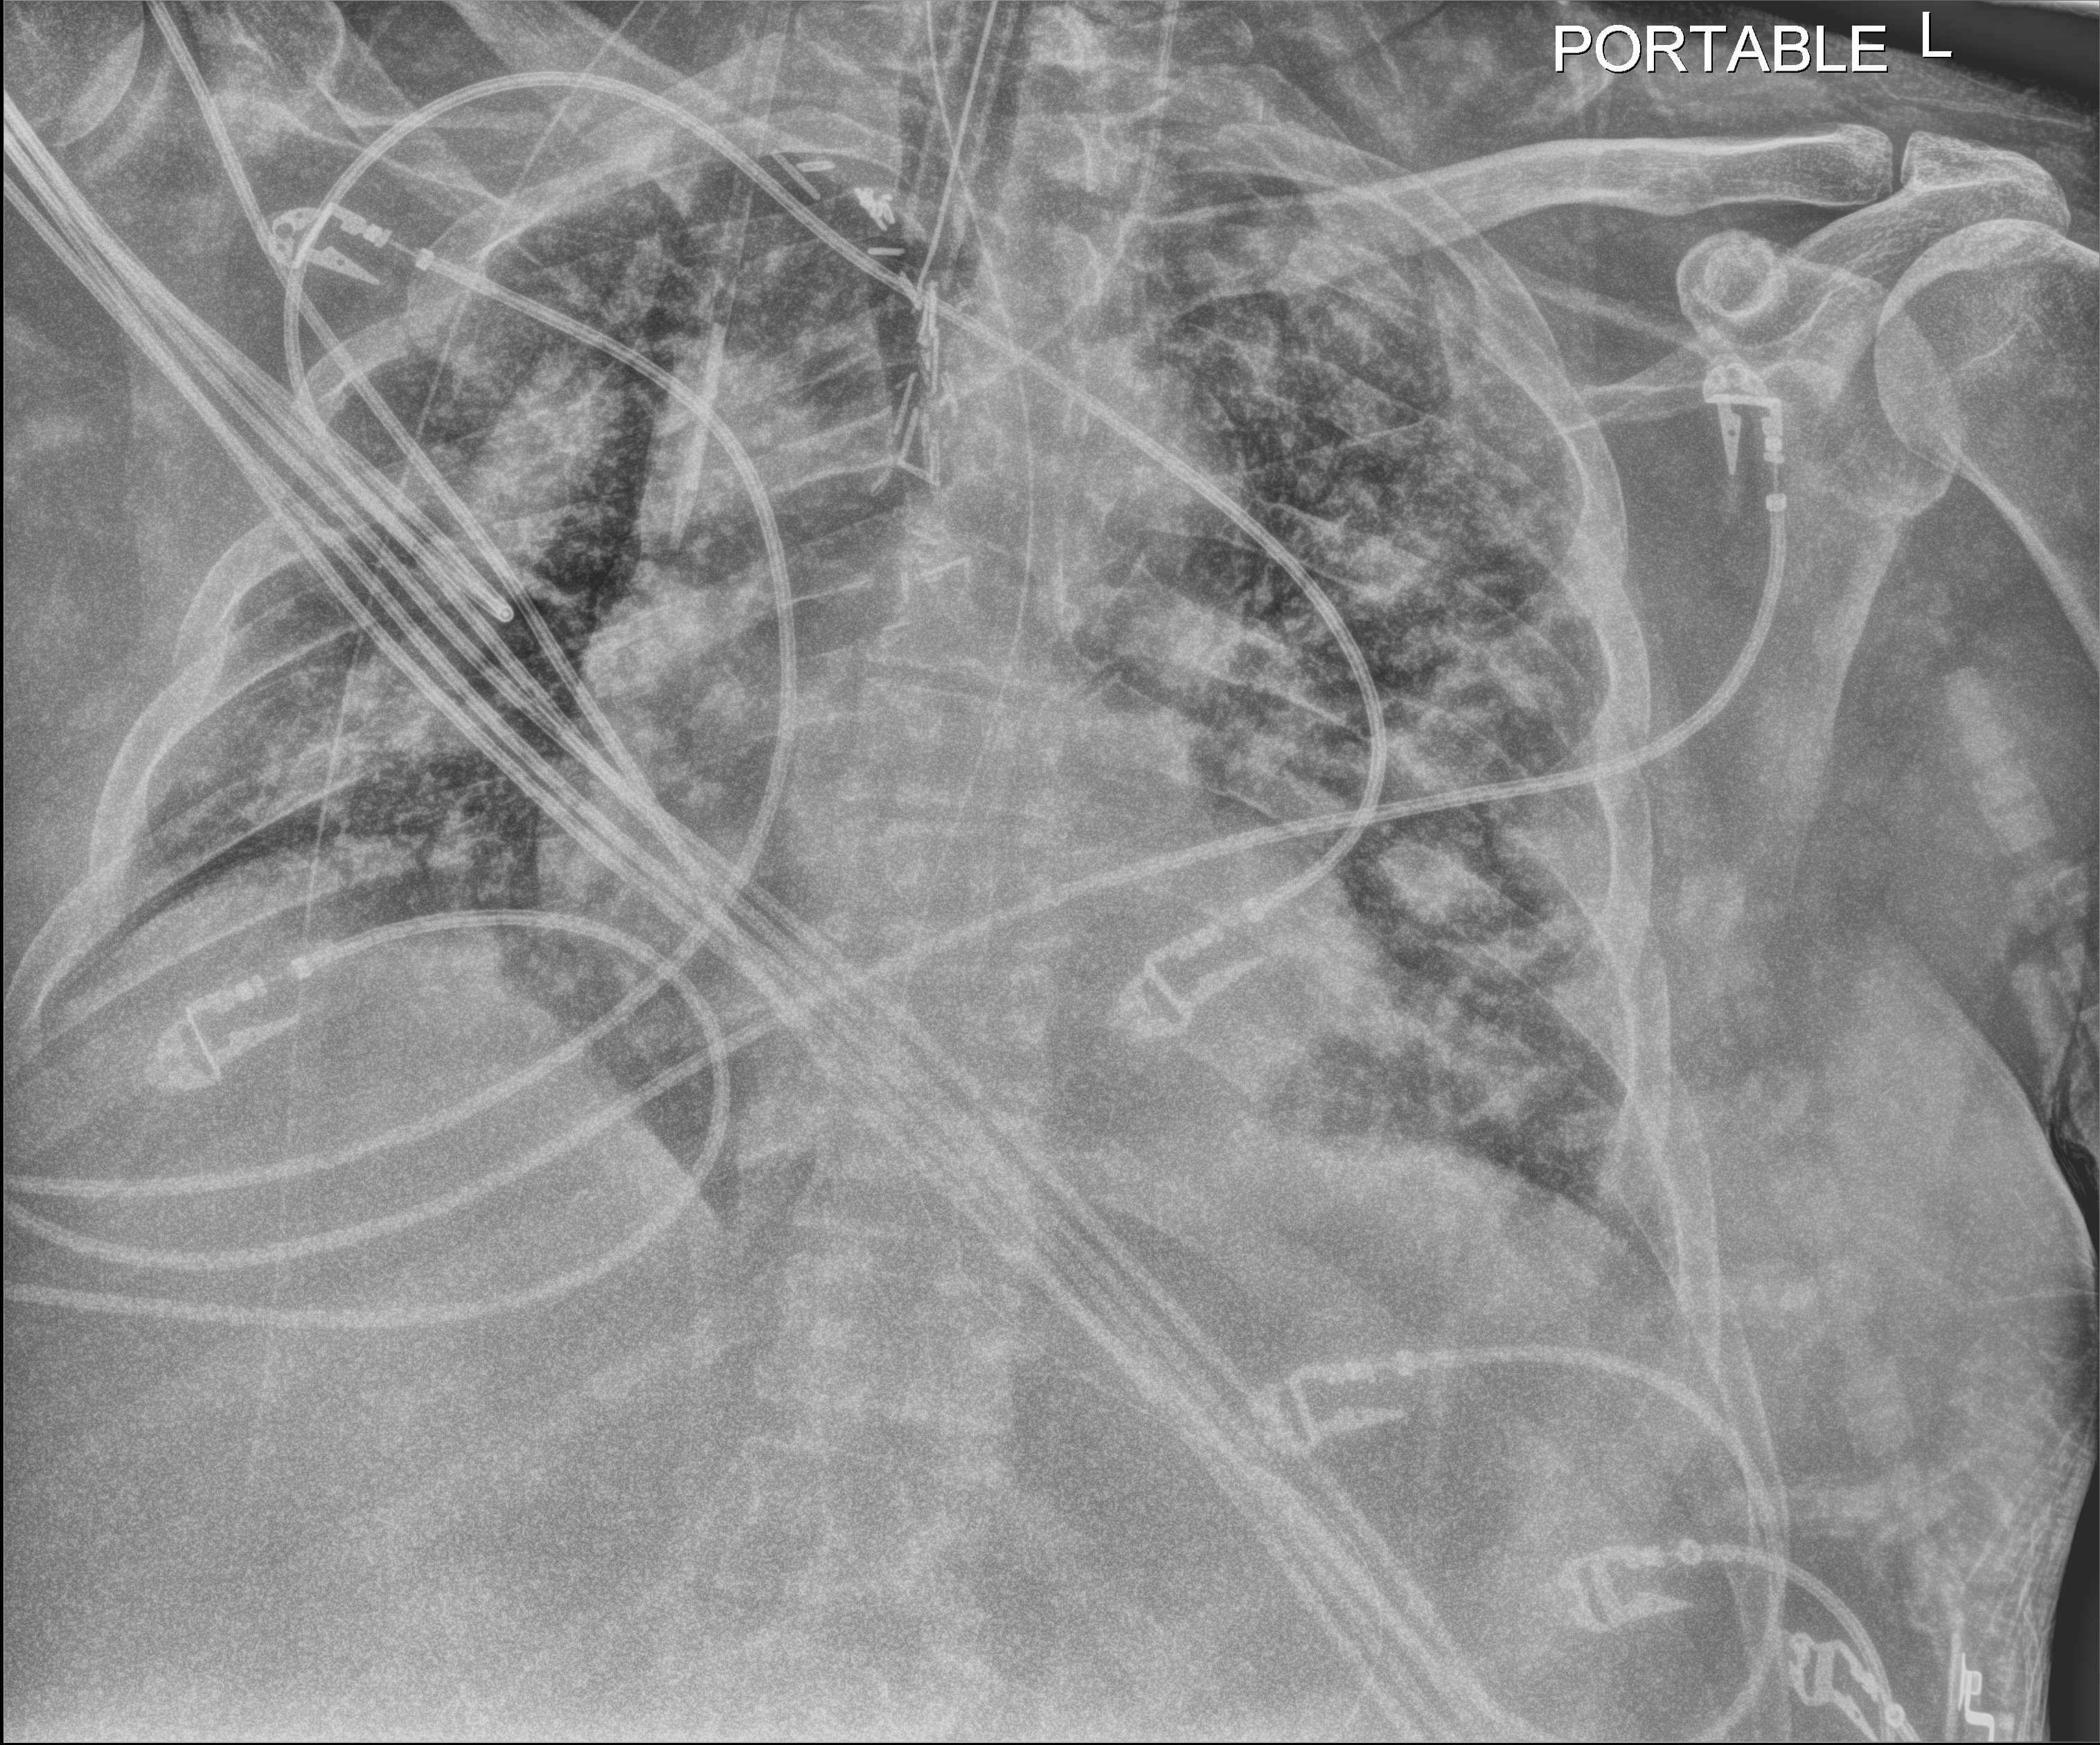
Bedside chest radiograph (digital radiography), anteroposterior (AP) projection. Patient hospitalised with COVID-19, aged 18–59 years.
Admission-level facts for this patient (not findings on this image; timing relative to this image not recorded):
- admitted to intensive care during this hospital stay: yes
- mechanically ventilated during this hospital stay: yes